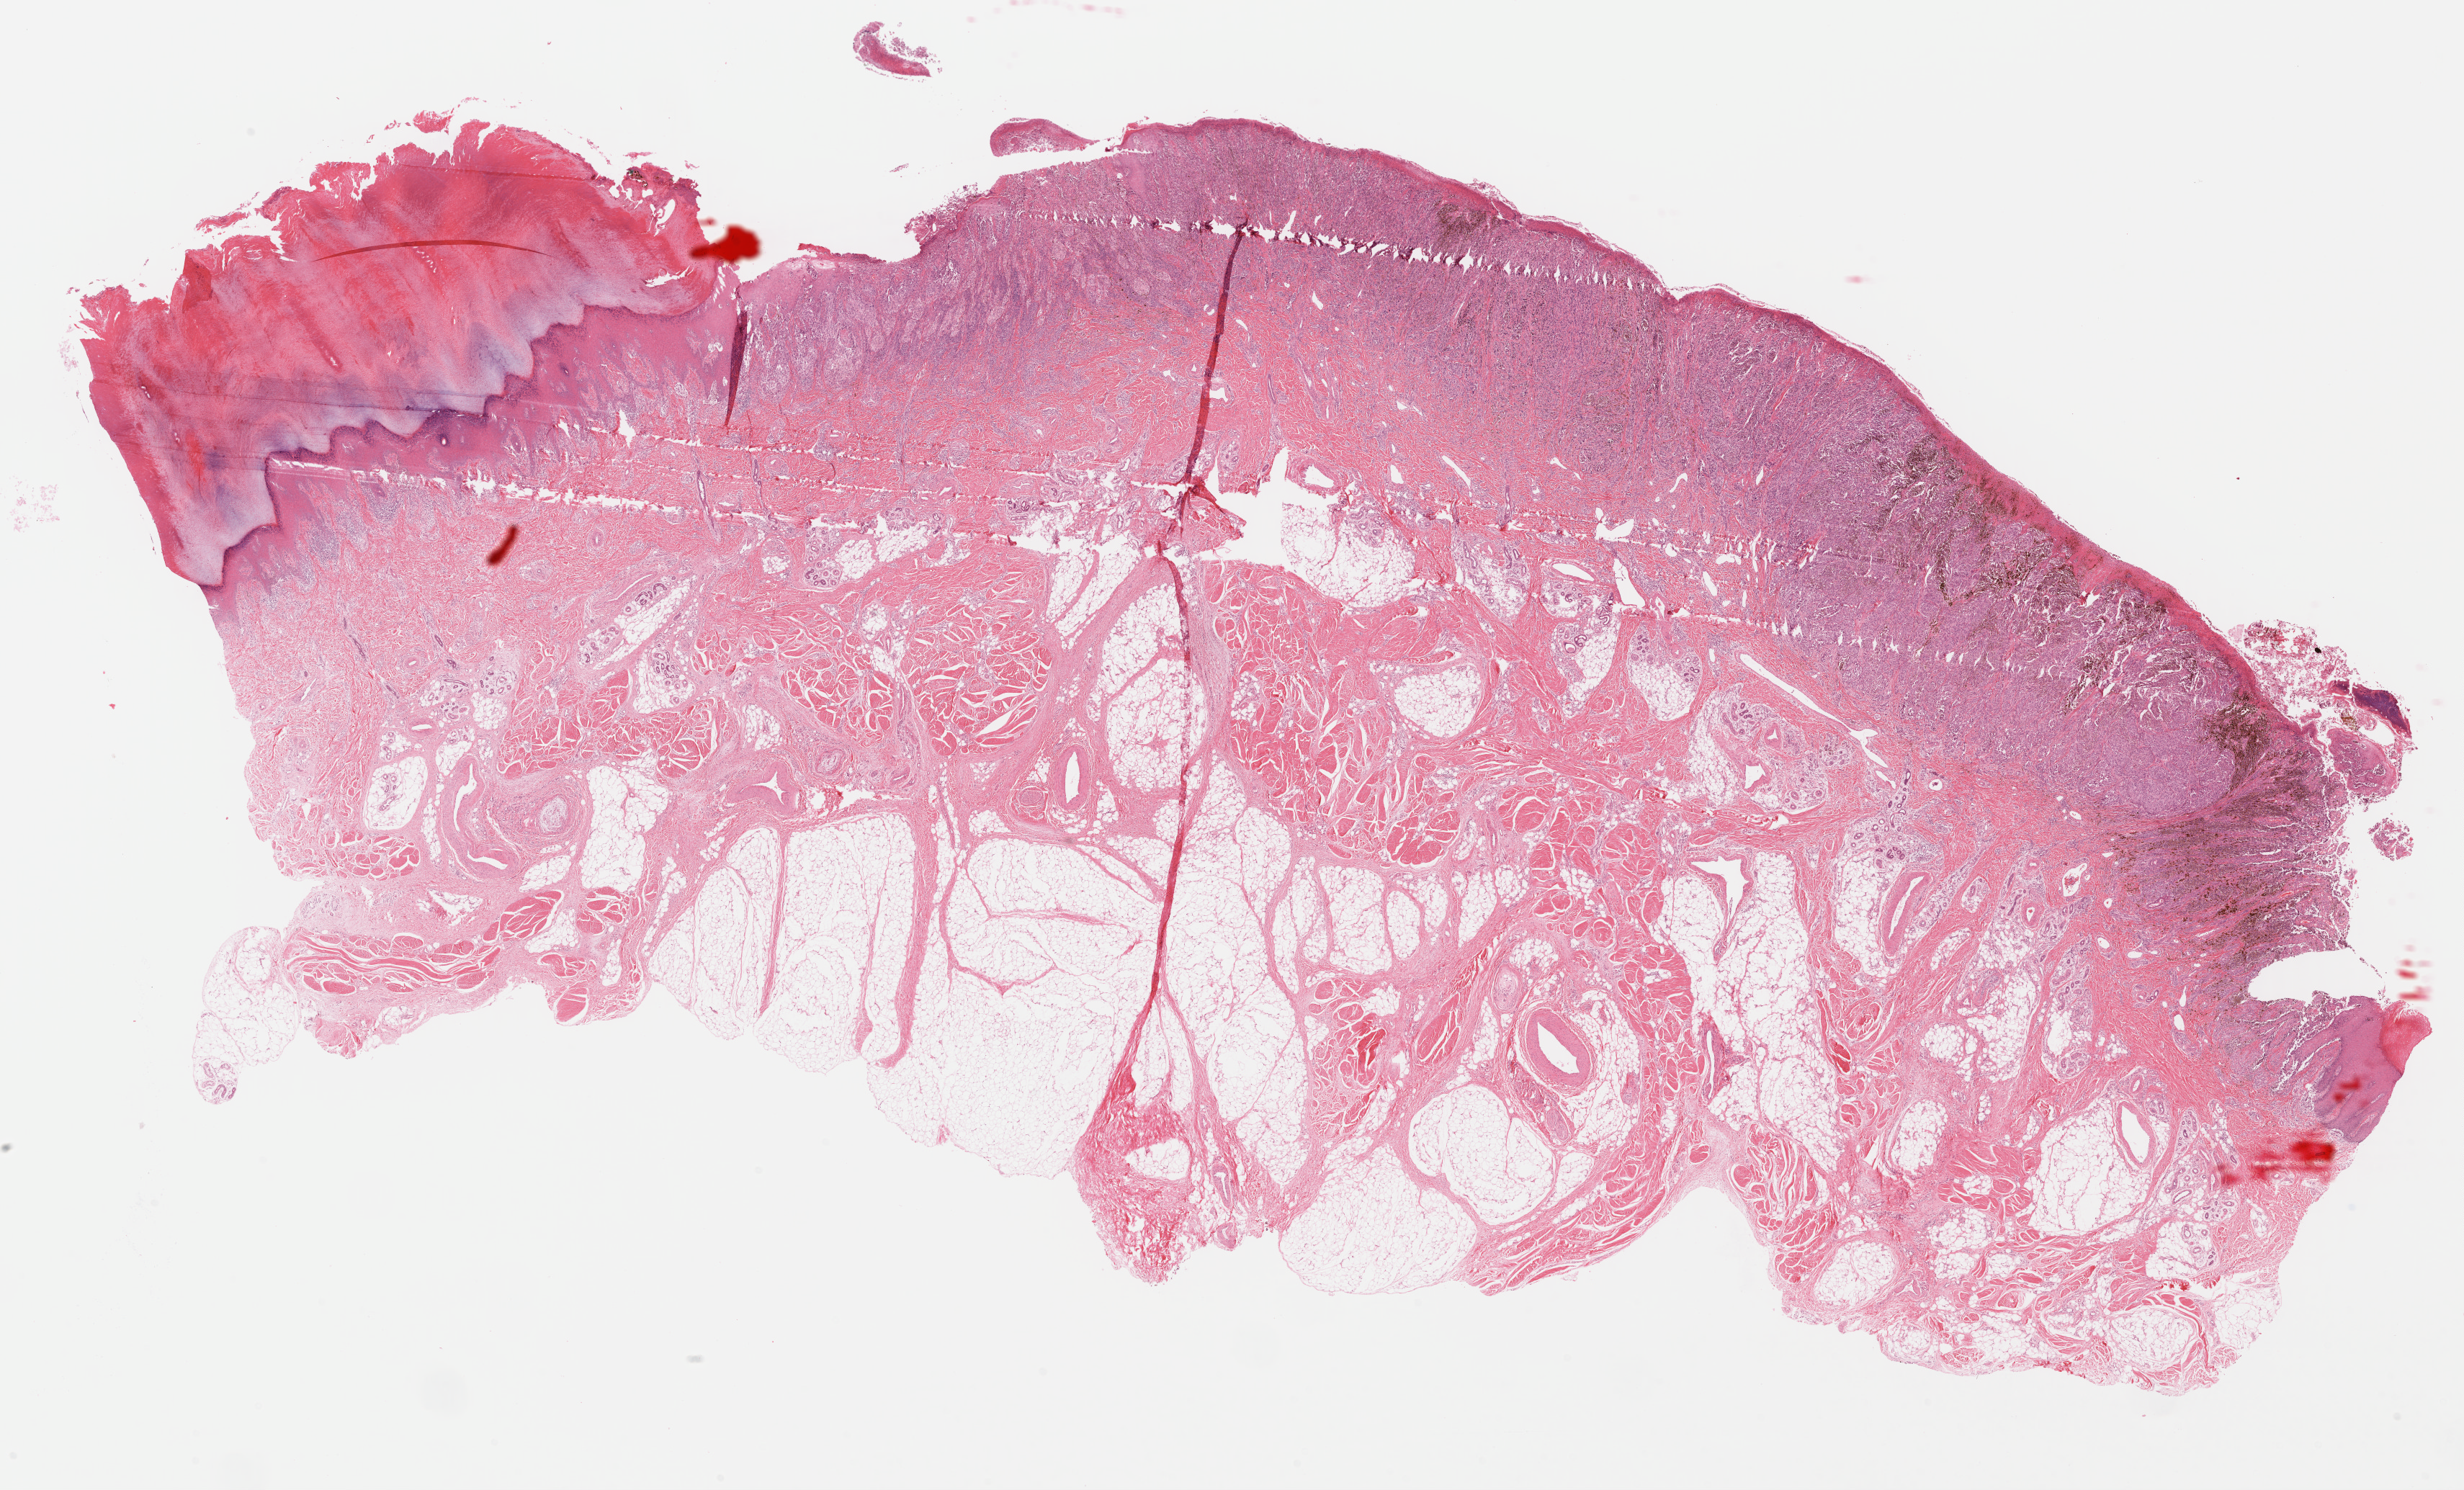
H&E whole-slide image, whole scanned area (about 26.9 x 16.3 mm, slide scanned at 40x) shown as a low-resolution overview. Formalin-fixed paraffin-embedded (FFPE) diagnostic section. Skin, primary tumour sample. Patient: male, age at initial diagnosis 56 years.
• AJCC pathologic stage: IIIB (7th edition)
• pathologic diagnosis: Malignant melanoma, NOS